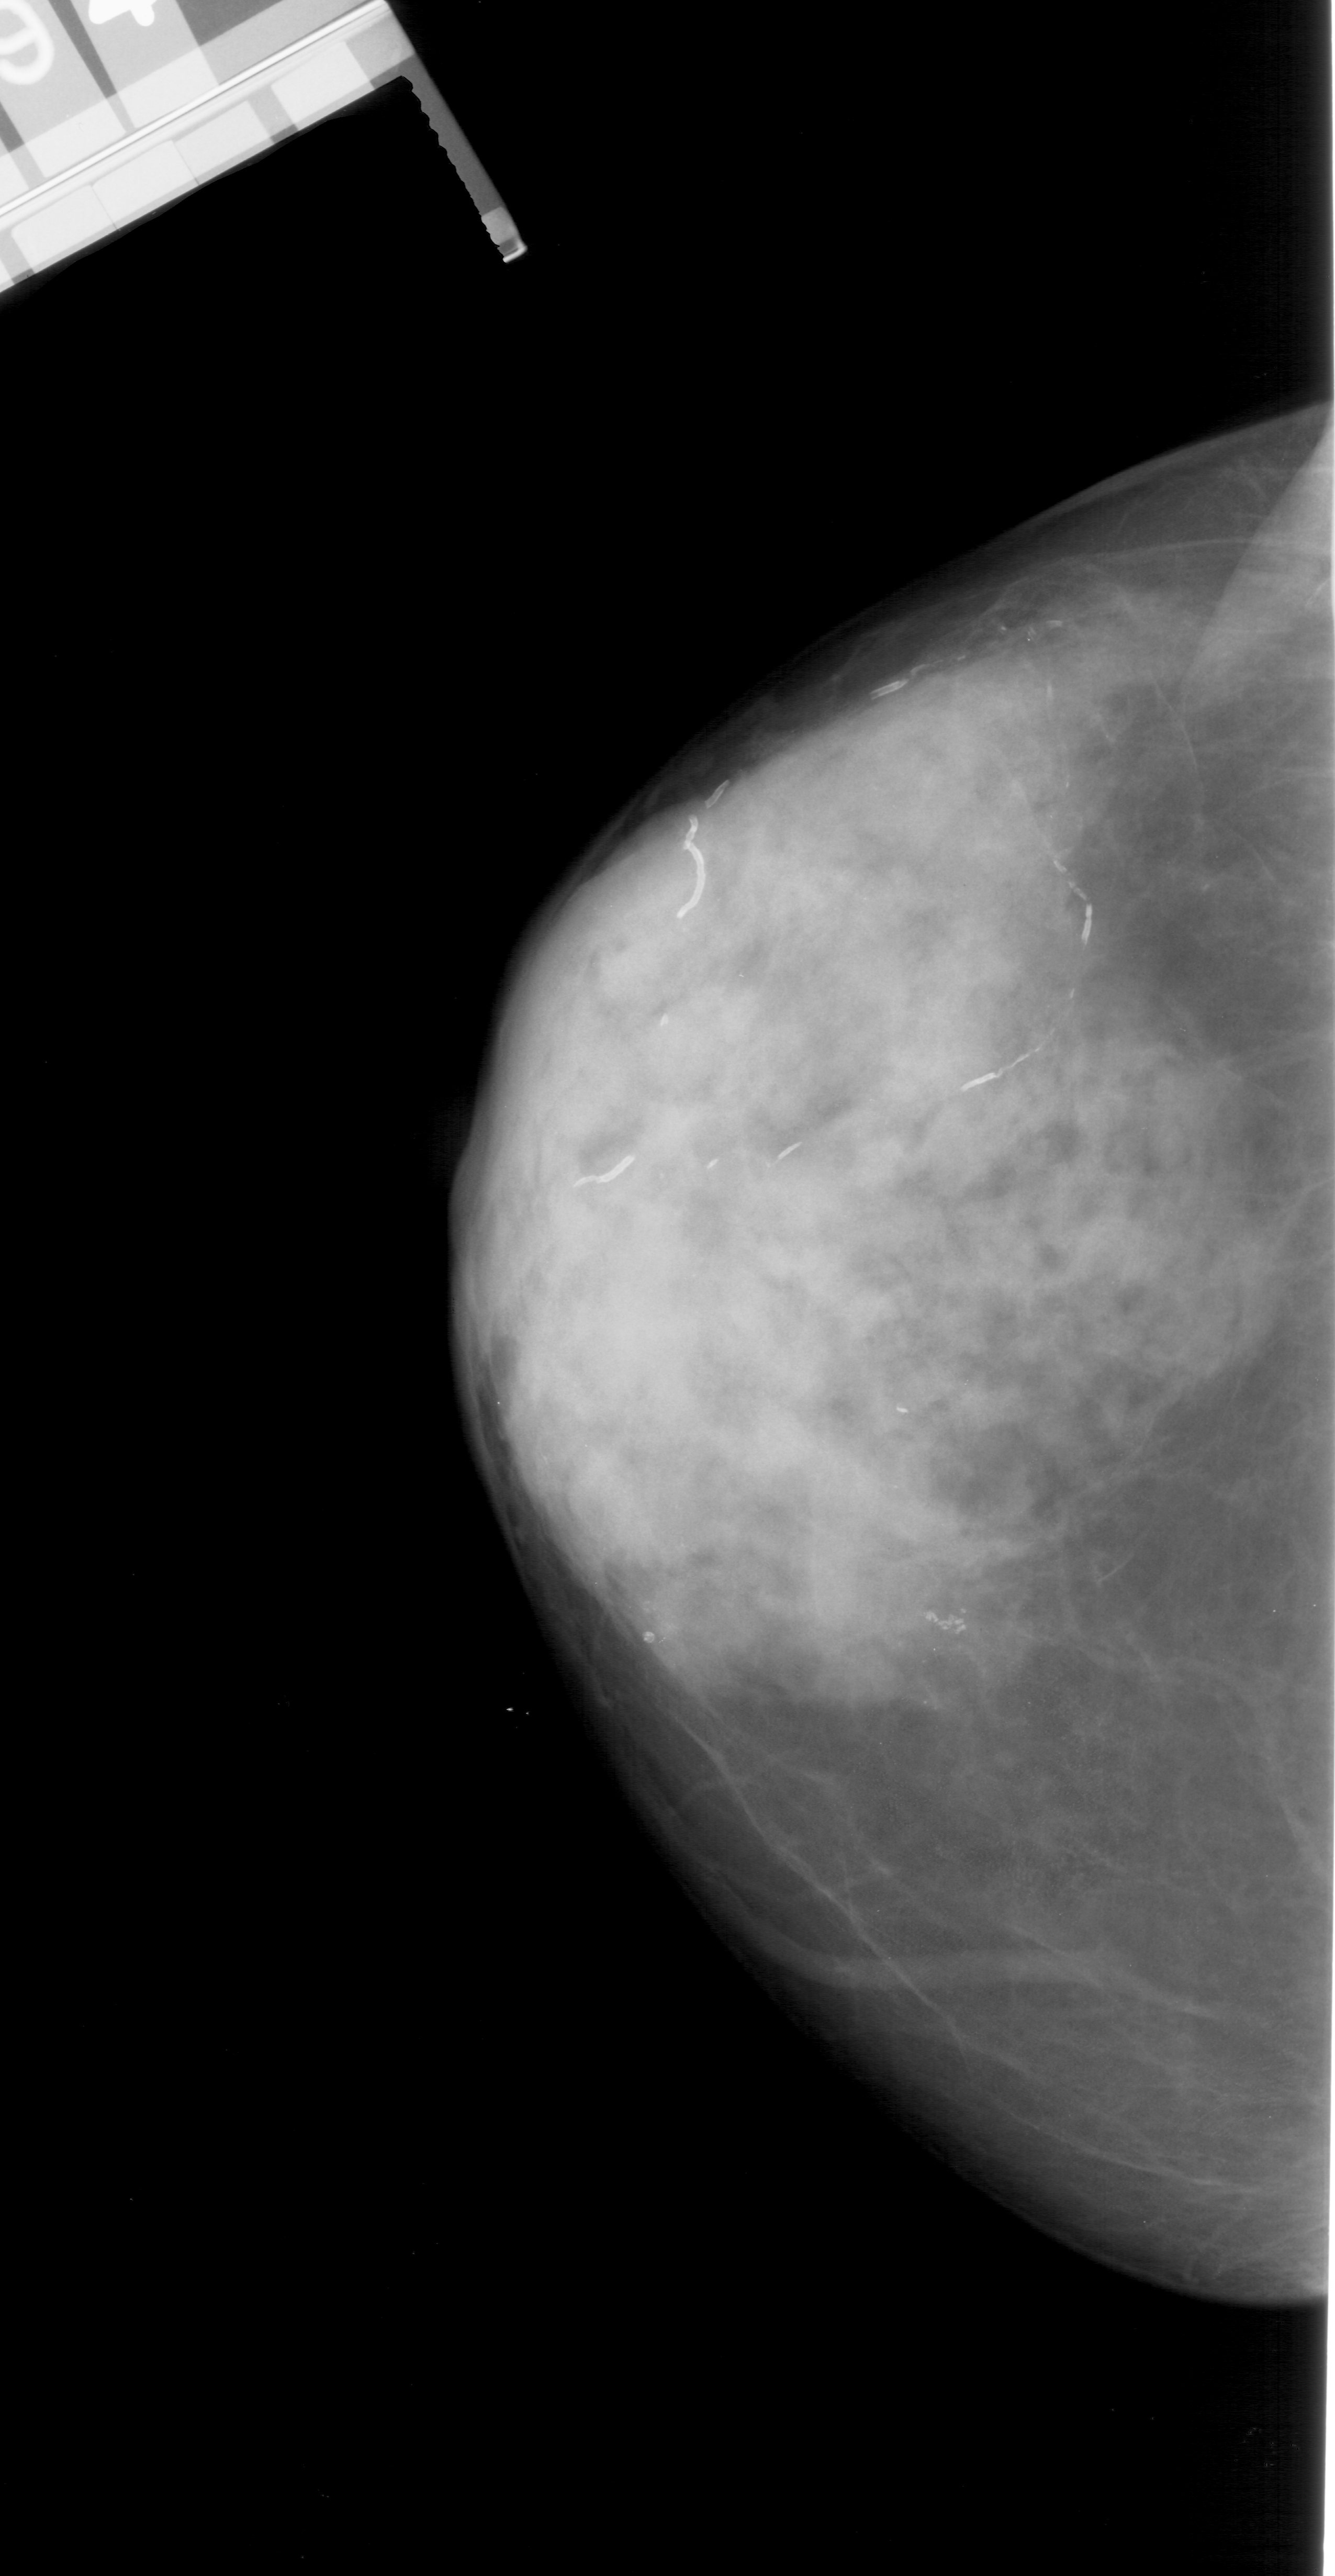
Scanned film-screen mammogram; left breast; craniocaudal (CC) view; breast composition: extremely dense (BI-RADS density category 4 of 4).
Calcifications, morphology pleomorphic, distribution clustered; BI-RADS assessment category 4; pathology (as recorded): malignant.